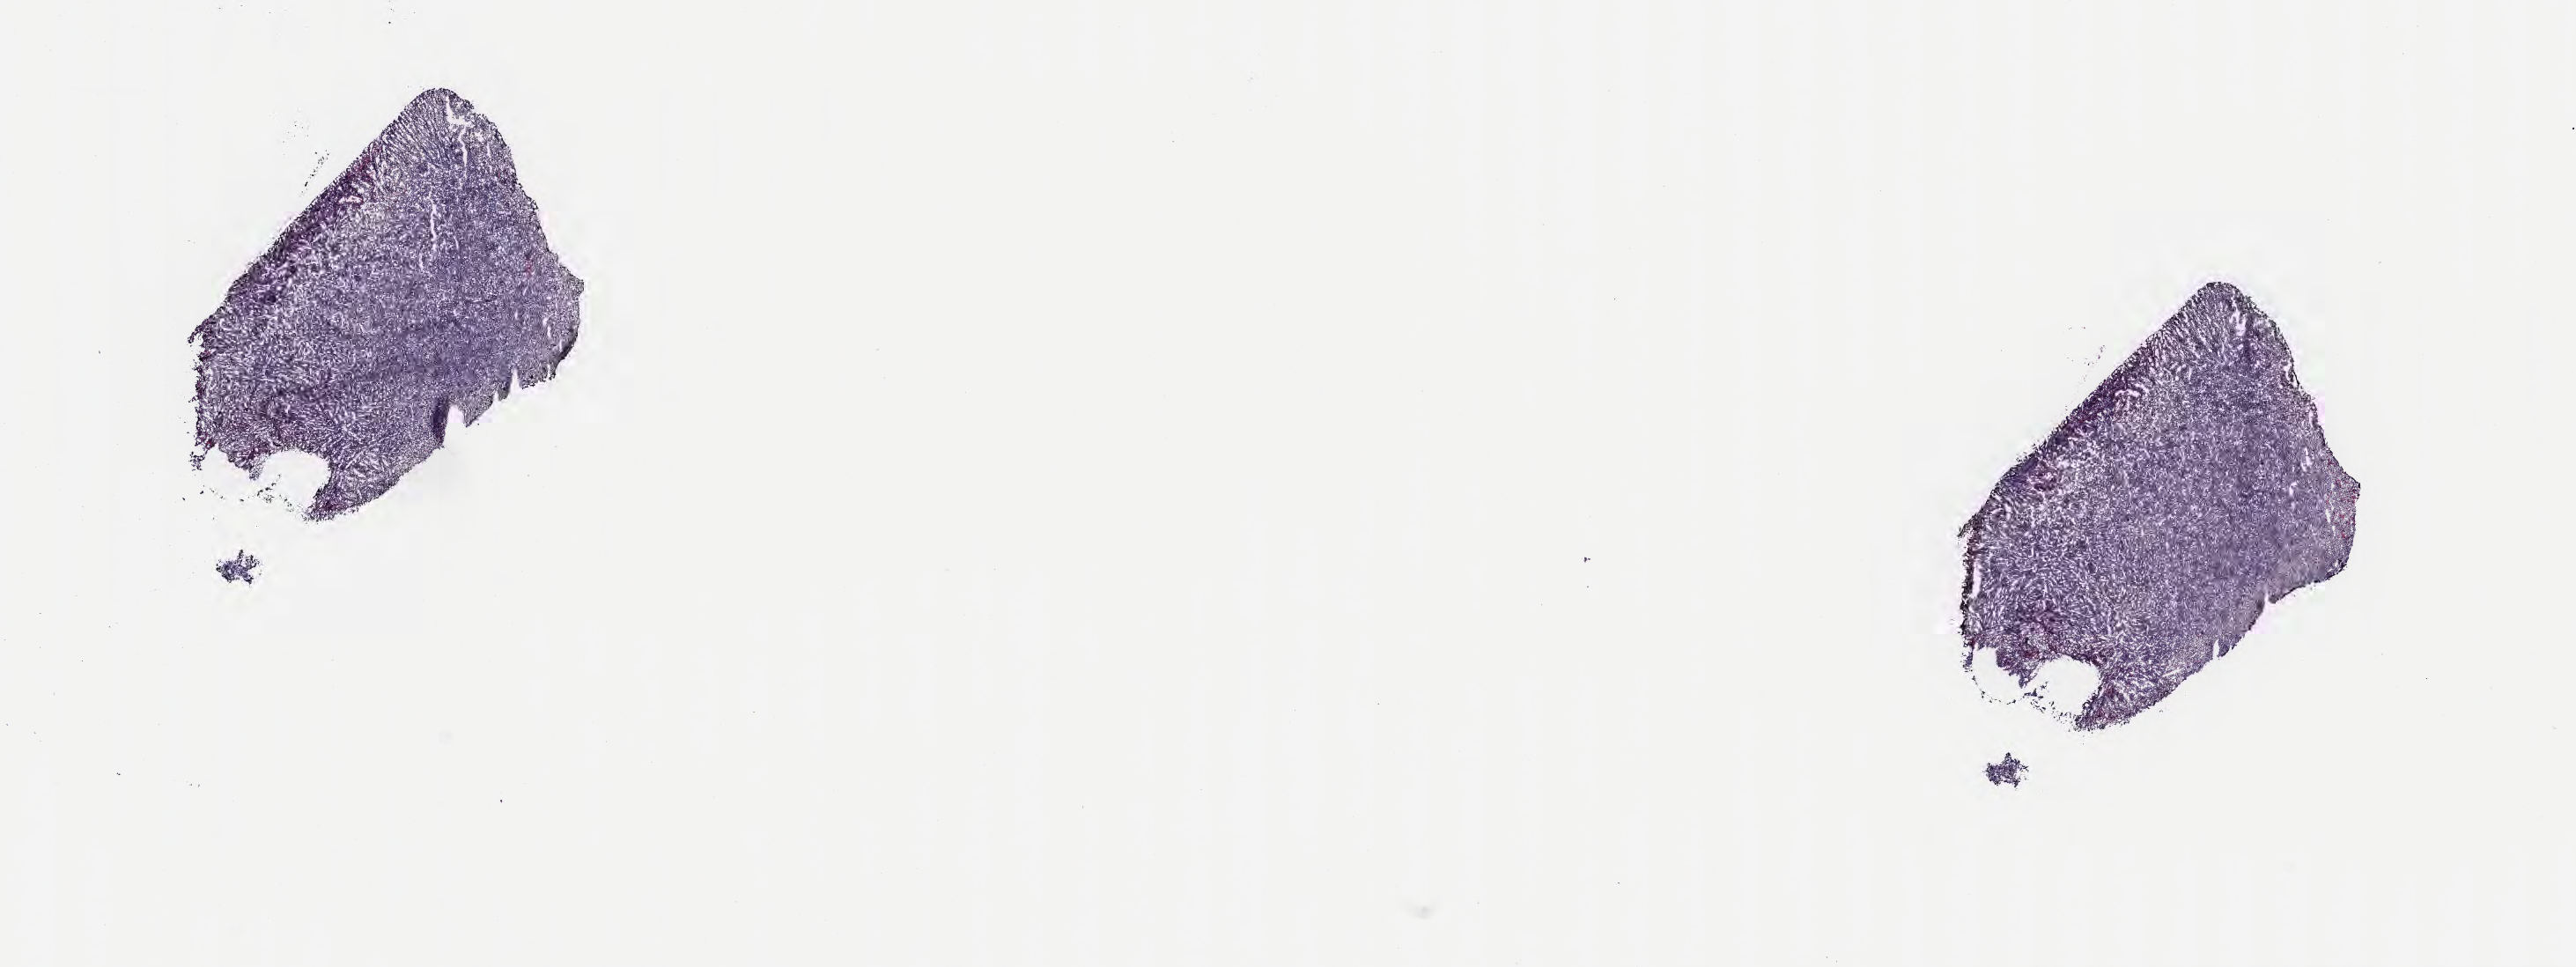
Digitized hematoxylin and eosin (H&E)-stained section — whole scanned area (about 23.7 x 8.9 mm) shown as a low-resolution overview; frozen section; specimen: primary tumor; site: lymph node of head and neck. Male, age 6 years at initial diagnosis.
Diagnosis: Burkitt lymphoma, NOS.